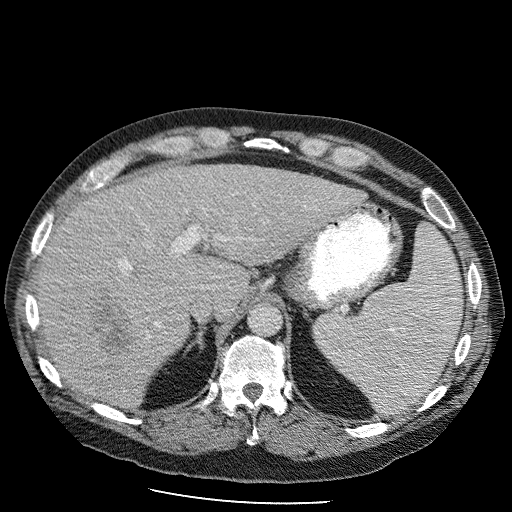
Contrast-enhanced abdominal CT (liver protocol), one axial slice; position 72 of 98 along the scan axis; reconstruction kernel STANDARD; 120 kVp; soft-tissue window (W 400 / L 40 HU); 512 × 512 image matrix. Case-level facts recorded for this patient, not image findings: diagnosis: hepatocellular carcinoma (patient treated with transarterial chemoembolisation; whether this scan precedes or follows treatment is not stated here); TNM stage (as recorded): Stage-II; Child-Pugh class: B; tumour differentiation: moderately differentiated; tumour nodularity: uninodular.
Outlined on this slice (semi-automatically segmented with operator editing):
- liver parenchyma outside the tumour (the mass and vessels are separate outlines, so this box may not span the whole liver): bounding box [x1, y1, x2, y2] px = [36, 164, 363, 408]
- mass: [77, 288, 139, 359]
- liver vessels: [120, 227, 221, 325]